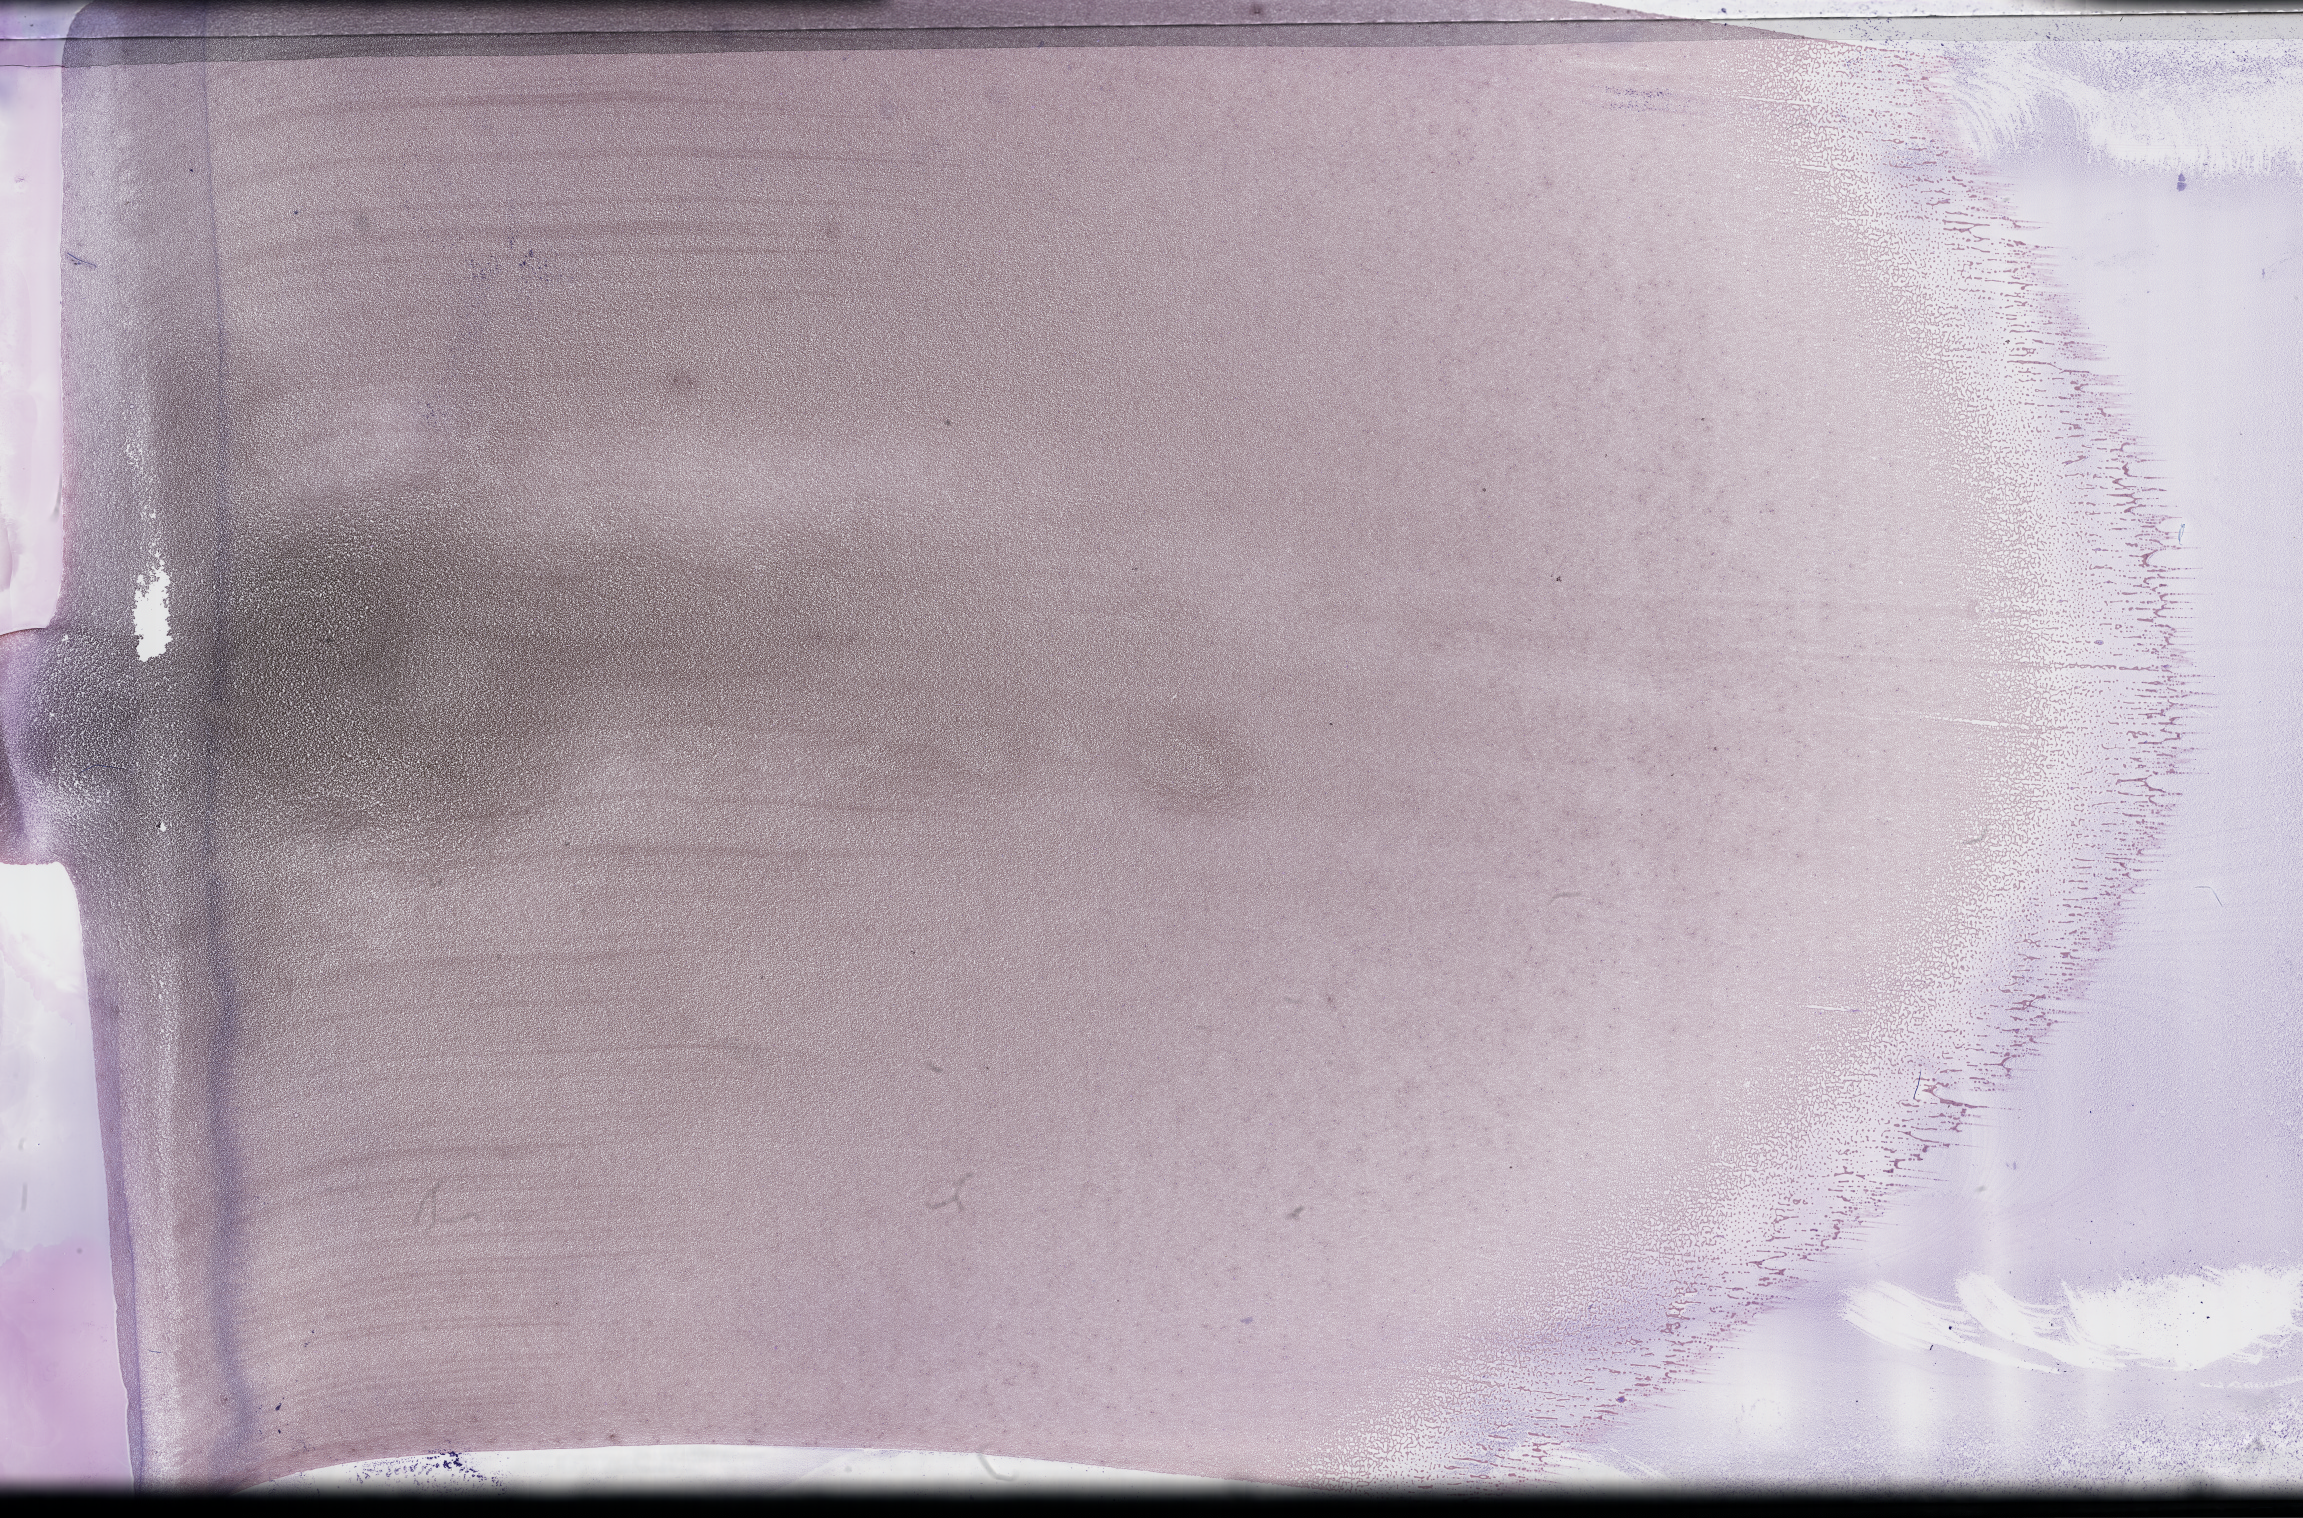
Wright–Giemsa-stained whole blood smear, whole-slide image — whole scanned area (about 37.2 x 24.5 mm) shown as a low-resolution overview; smear from an EDTA sample. Patient sex: male.
From a patient with: Plasma Cell Myeloma.